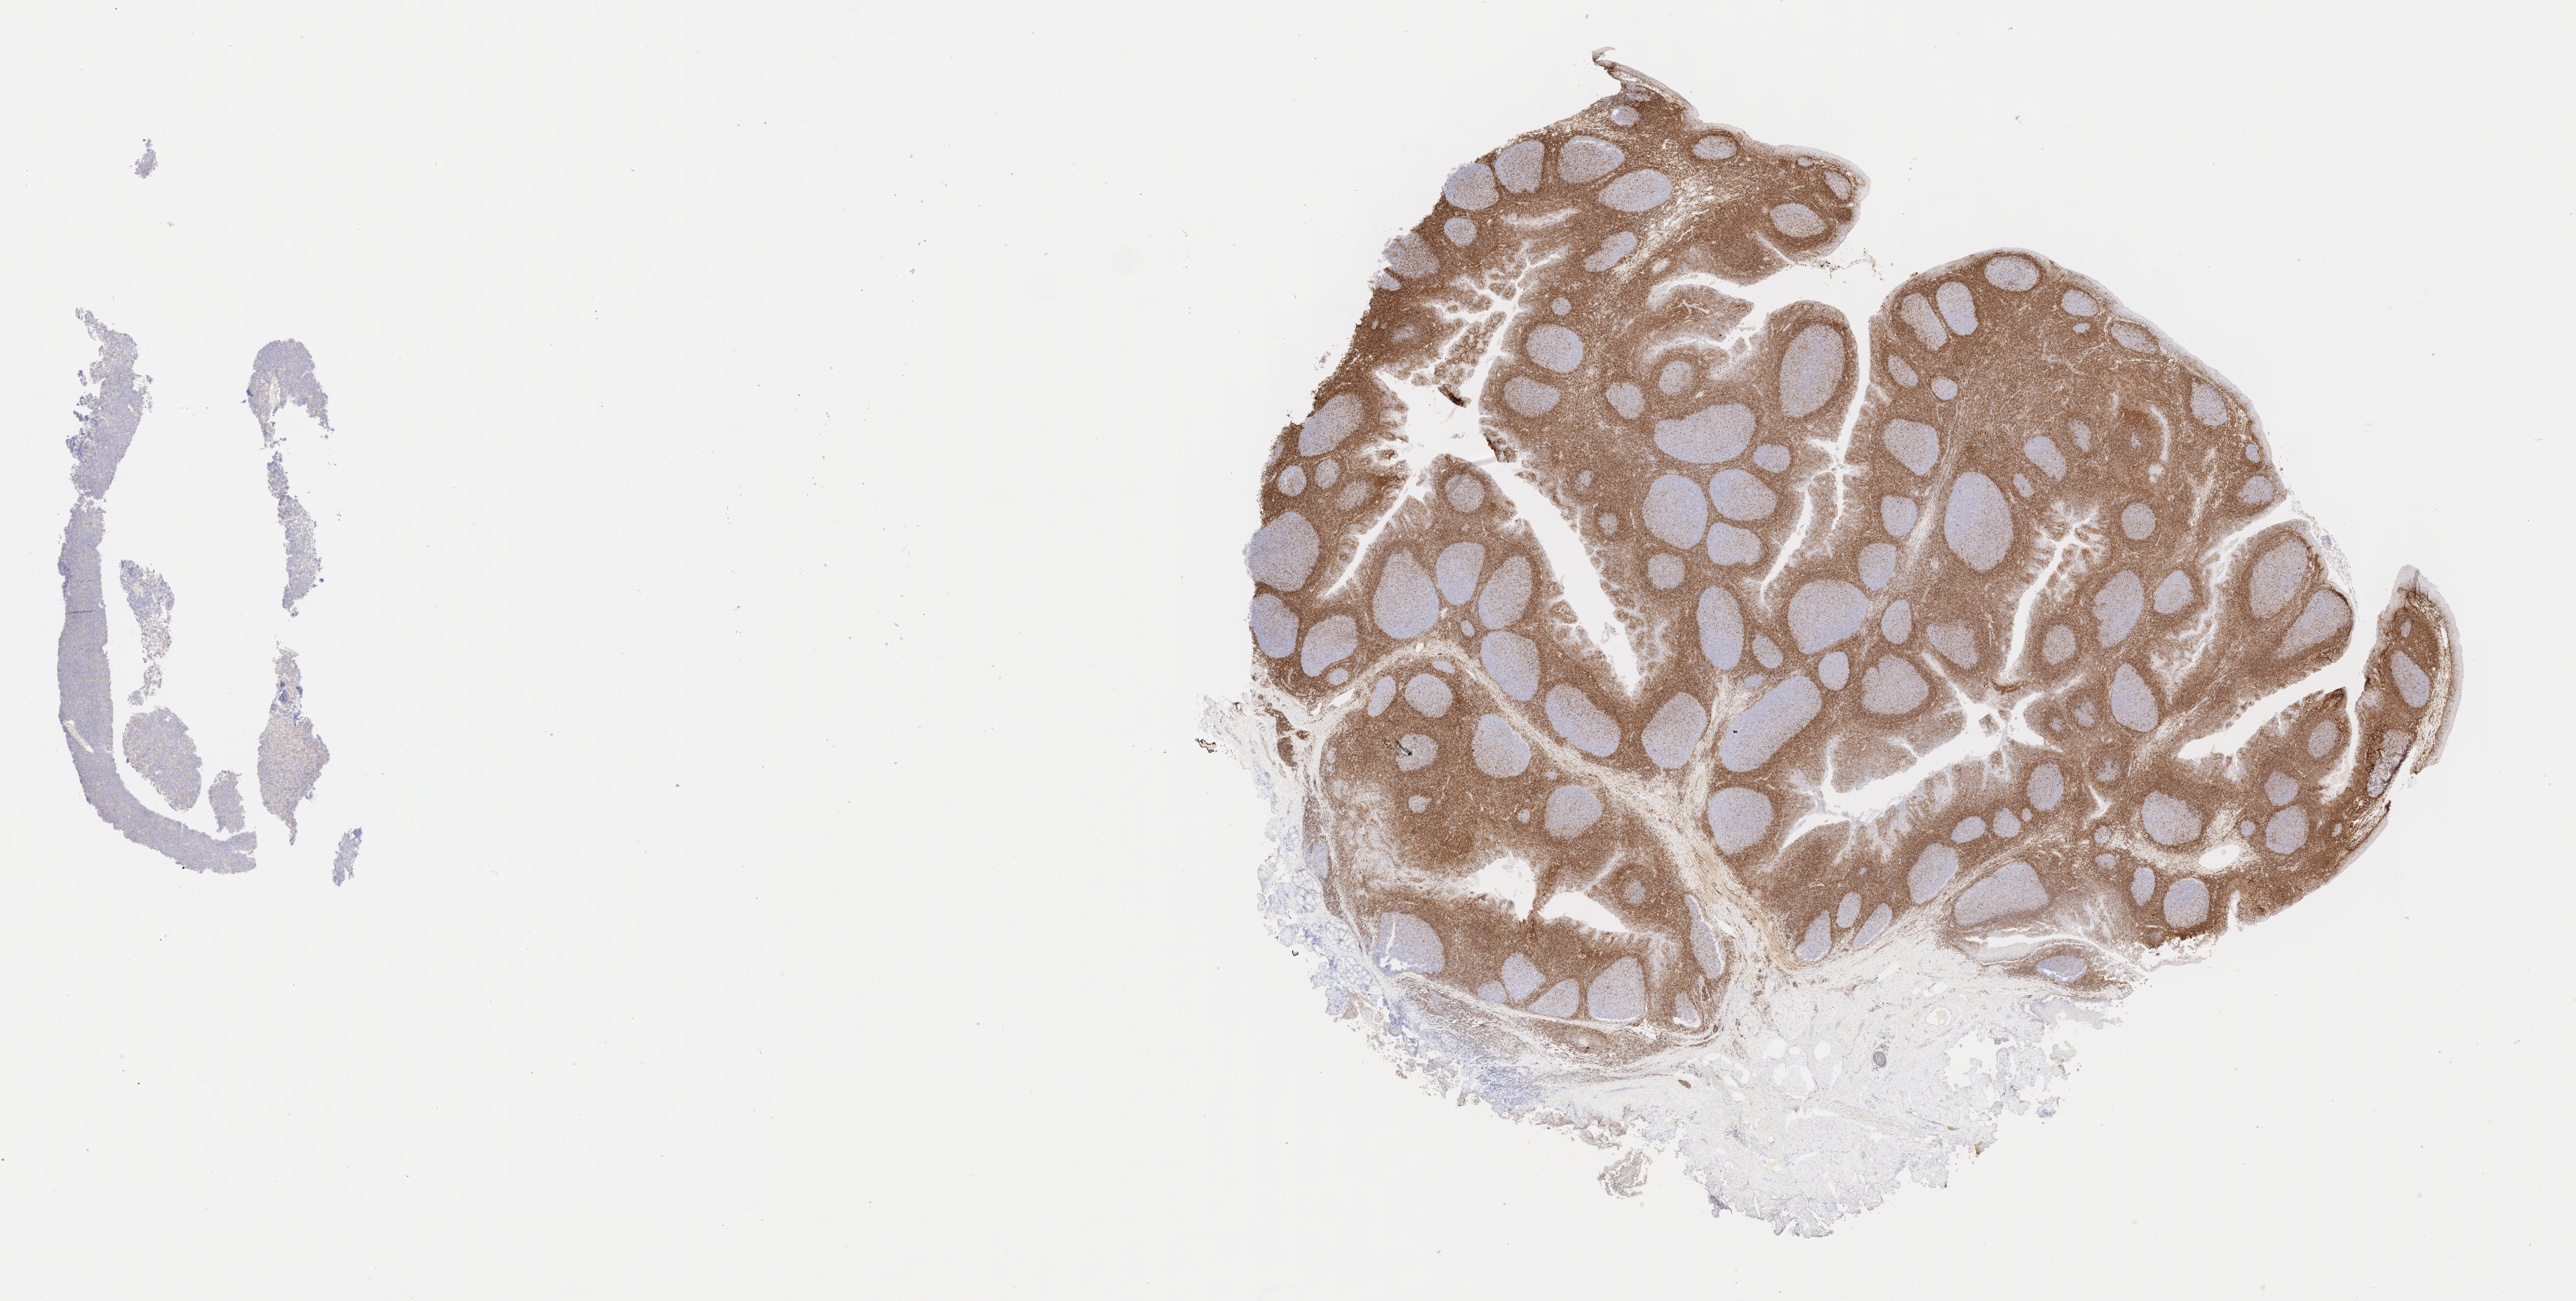
IHC for BCL2, whole-slide image — shown as a low-resolution overview of the whole scanned area (about 29.7 x 15.0 mm), tumor tissue. Female patient, age 10 years.
Diagnosis: Burkitt lymphoma, NOS.